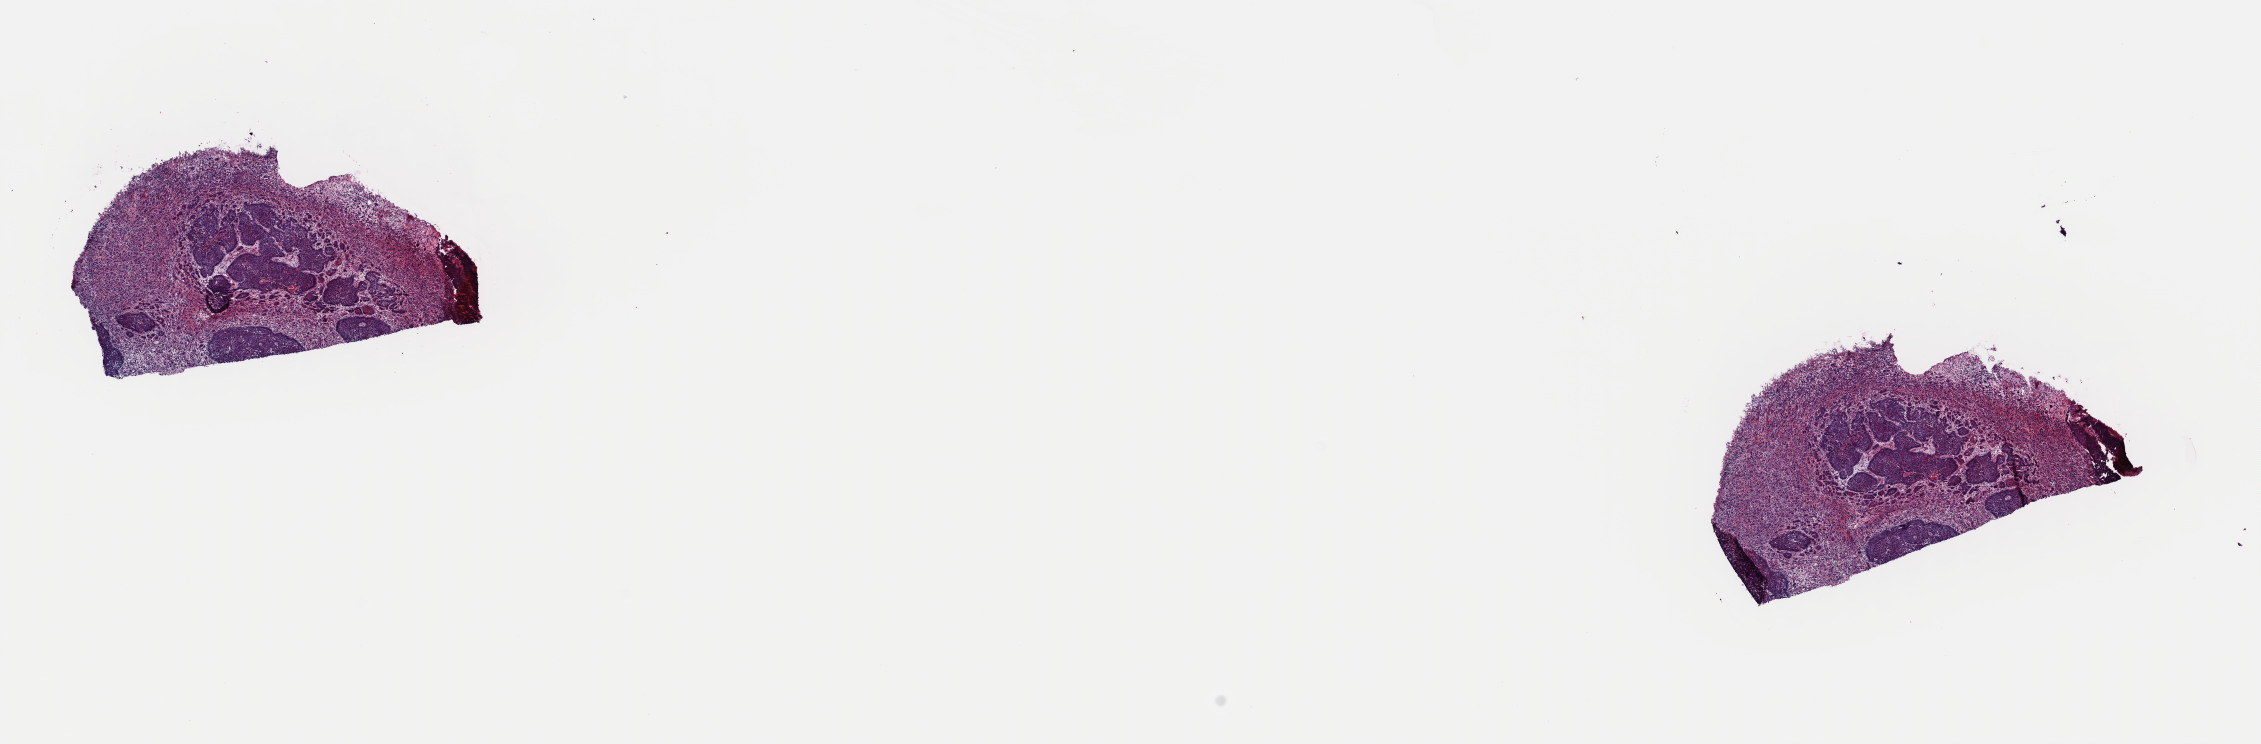
Digitized H&E tissue section (whole slide), shown as a low-resolution overview of the whole scanned area (about 17.9 x 5.9 mm, slide scanned at 40x); frozen section from the top of the tissue portion; head and neck, primary tumour sample. Patient: male, age at initial diagnosis 59 years. Pathologist review of this section (percent, as recorded): tumour cells 100%, tumour nuclei 65%.
Diagnosis: Squamous cell carcinoma, NOS (floor of mouth, NOS).